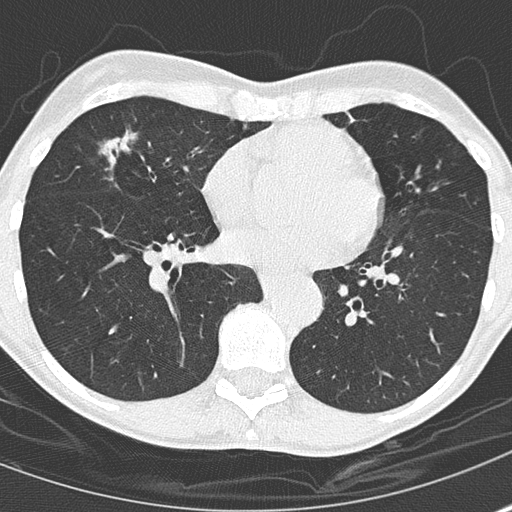
Chest CT (low-dose screening protocol), one axial image. Second annual screen. Lung window (W 1500 / L -600 HU). 2 mm slice thickness. 120 kVp. Slice 102 of 167 in the series. Female, age 67 years at enrolment. Current smoker at enrolment.
• Lesion marked by an expert reader, bounding box [x1, y1, x2, y2] px = [83, 115, 185, 205].
• The screening reader recorded 2 non-calcified nodules or masses ≥4 mm on this exam; which of them this box marks is not recorded.
• Later outcome: lung cancer diagnosed 475 days after this screen — bronchiolo-alveolar adenocarcinoma, NOS, right middle lobe, well differentiated (G1), stage IA (AJCC 6th edition), 25 mm at pathology.